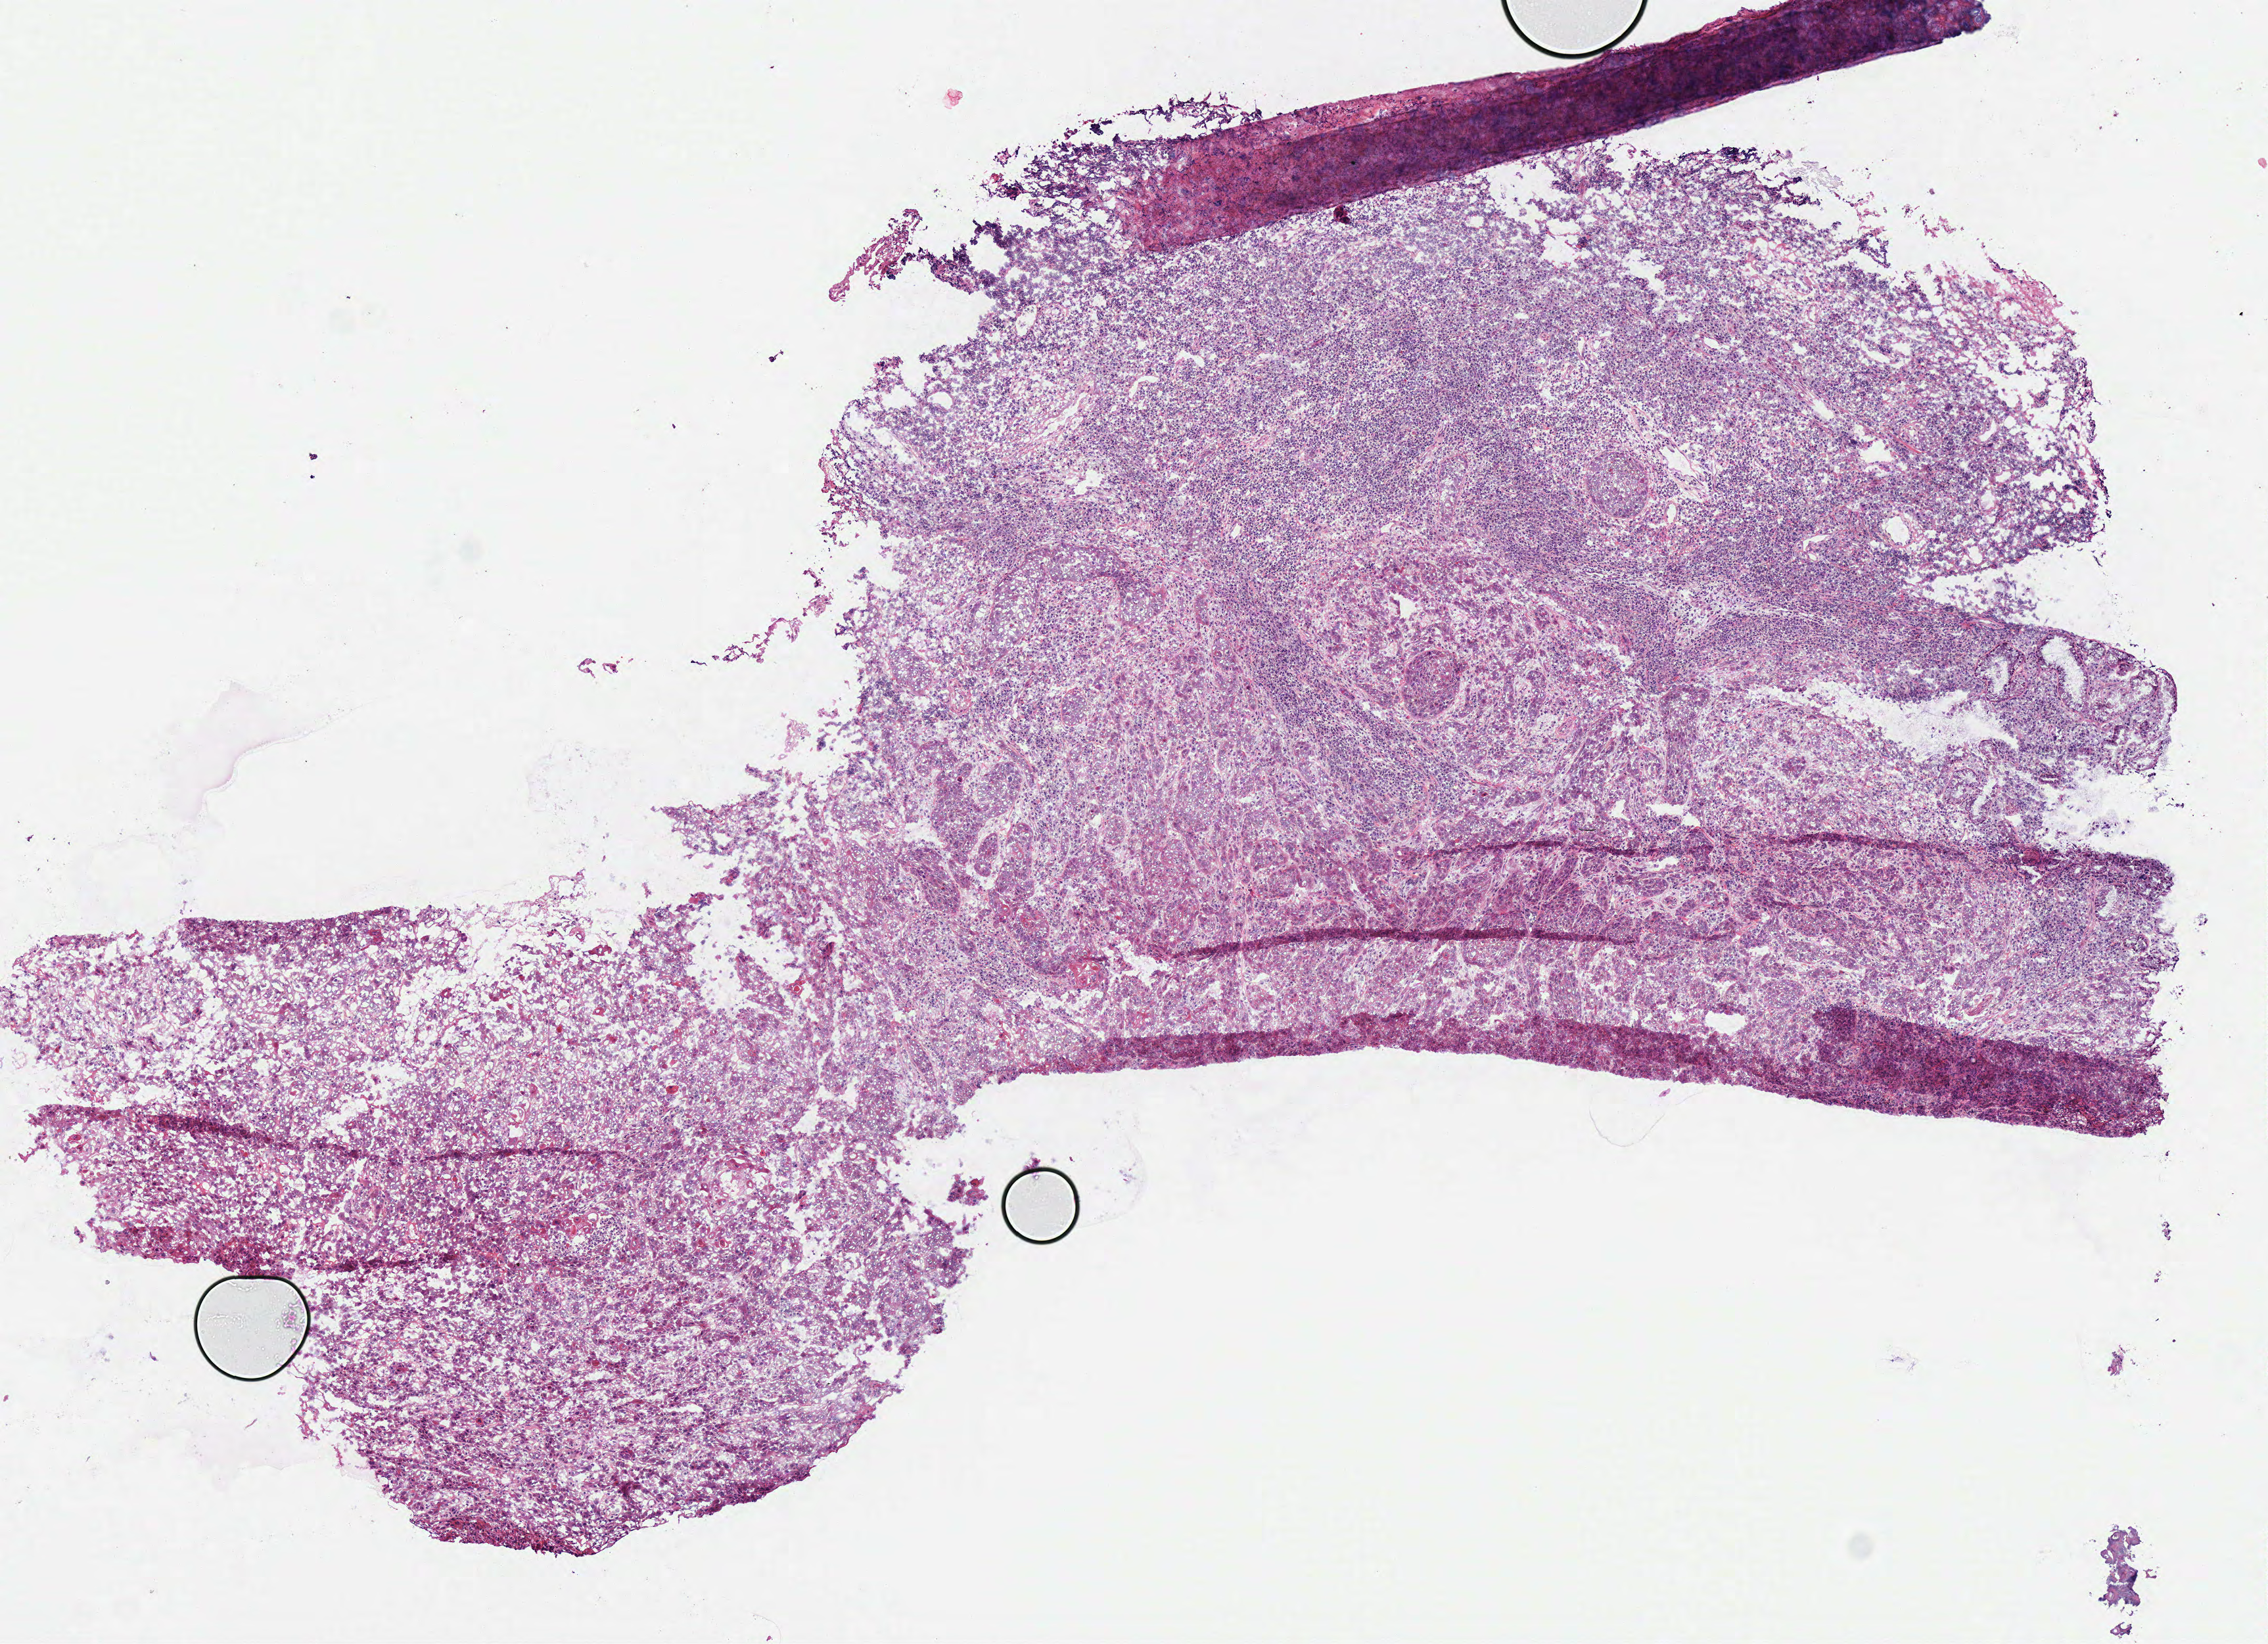
H&E whole-slide image, a low-resolution overview of the entire scanned area, about 6.8 x 4.9 mm (slide scanned at 40x). Frozen section from the bottom of the tissue portion. Primary tumour sample from the head and neck. Patient: female, age at initial diagnosis 60 years. Histologic grade: G2 (moderately differentiated). Composition of this section per pathologist review: tumour cells 95%, tumour nuclei 97%, normal cells 0%, stromal cells 3%, necrosis 2%. Inflammatory infiltration, as recorded: neutrophil infiltration 1%.
- laterality: left
- diagnosis: Squamous cell carcinoma, NOS